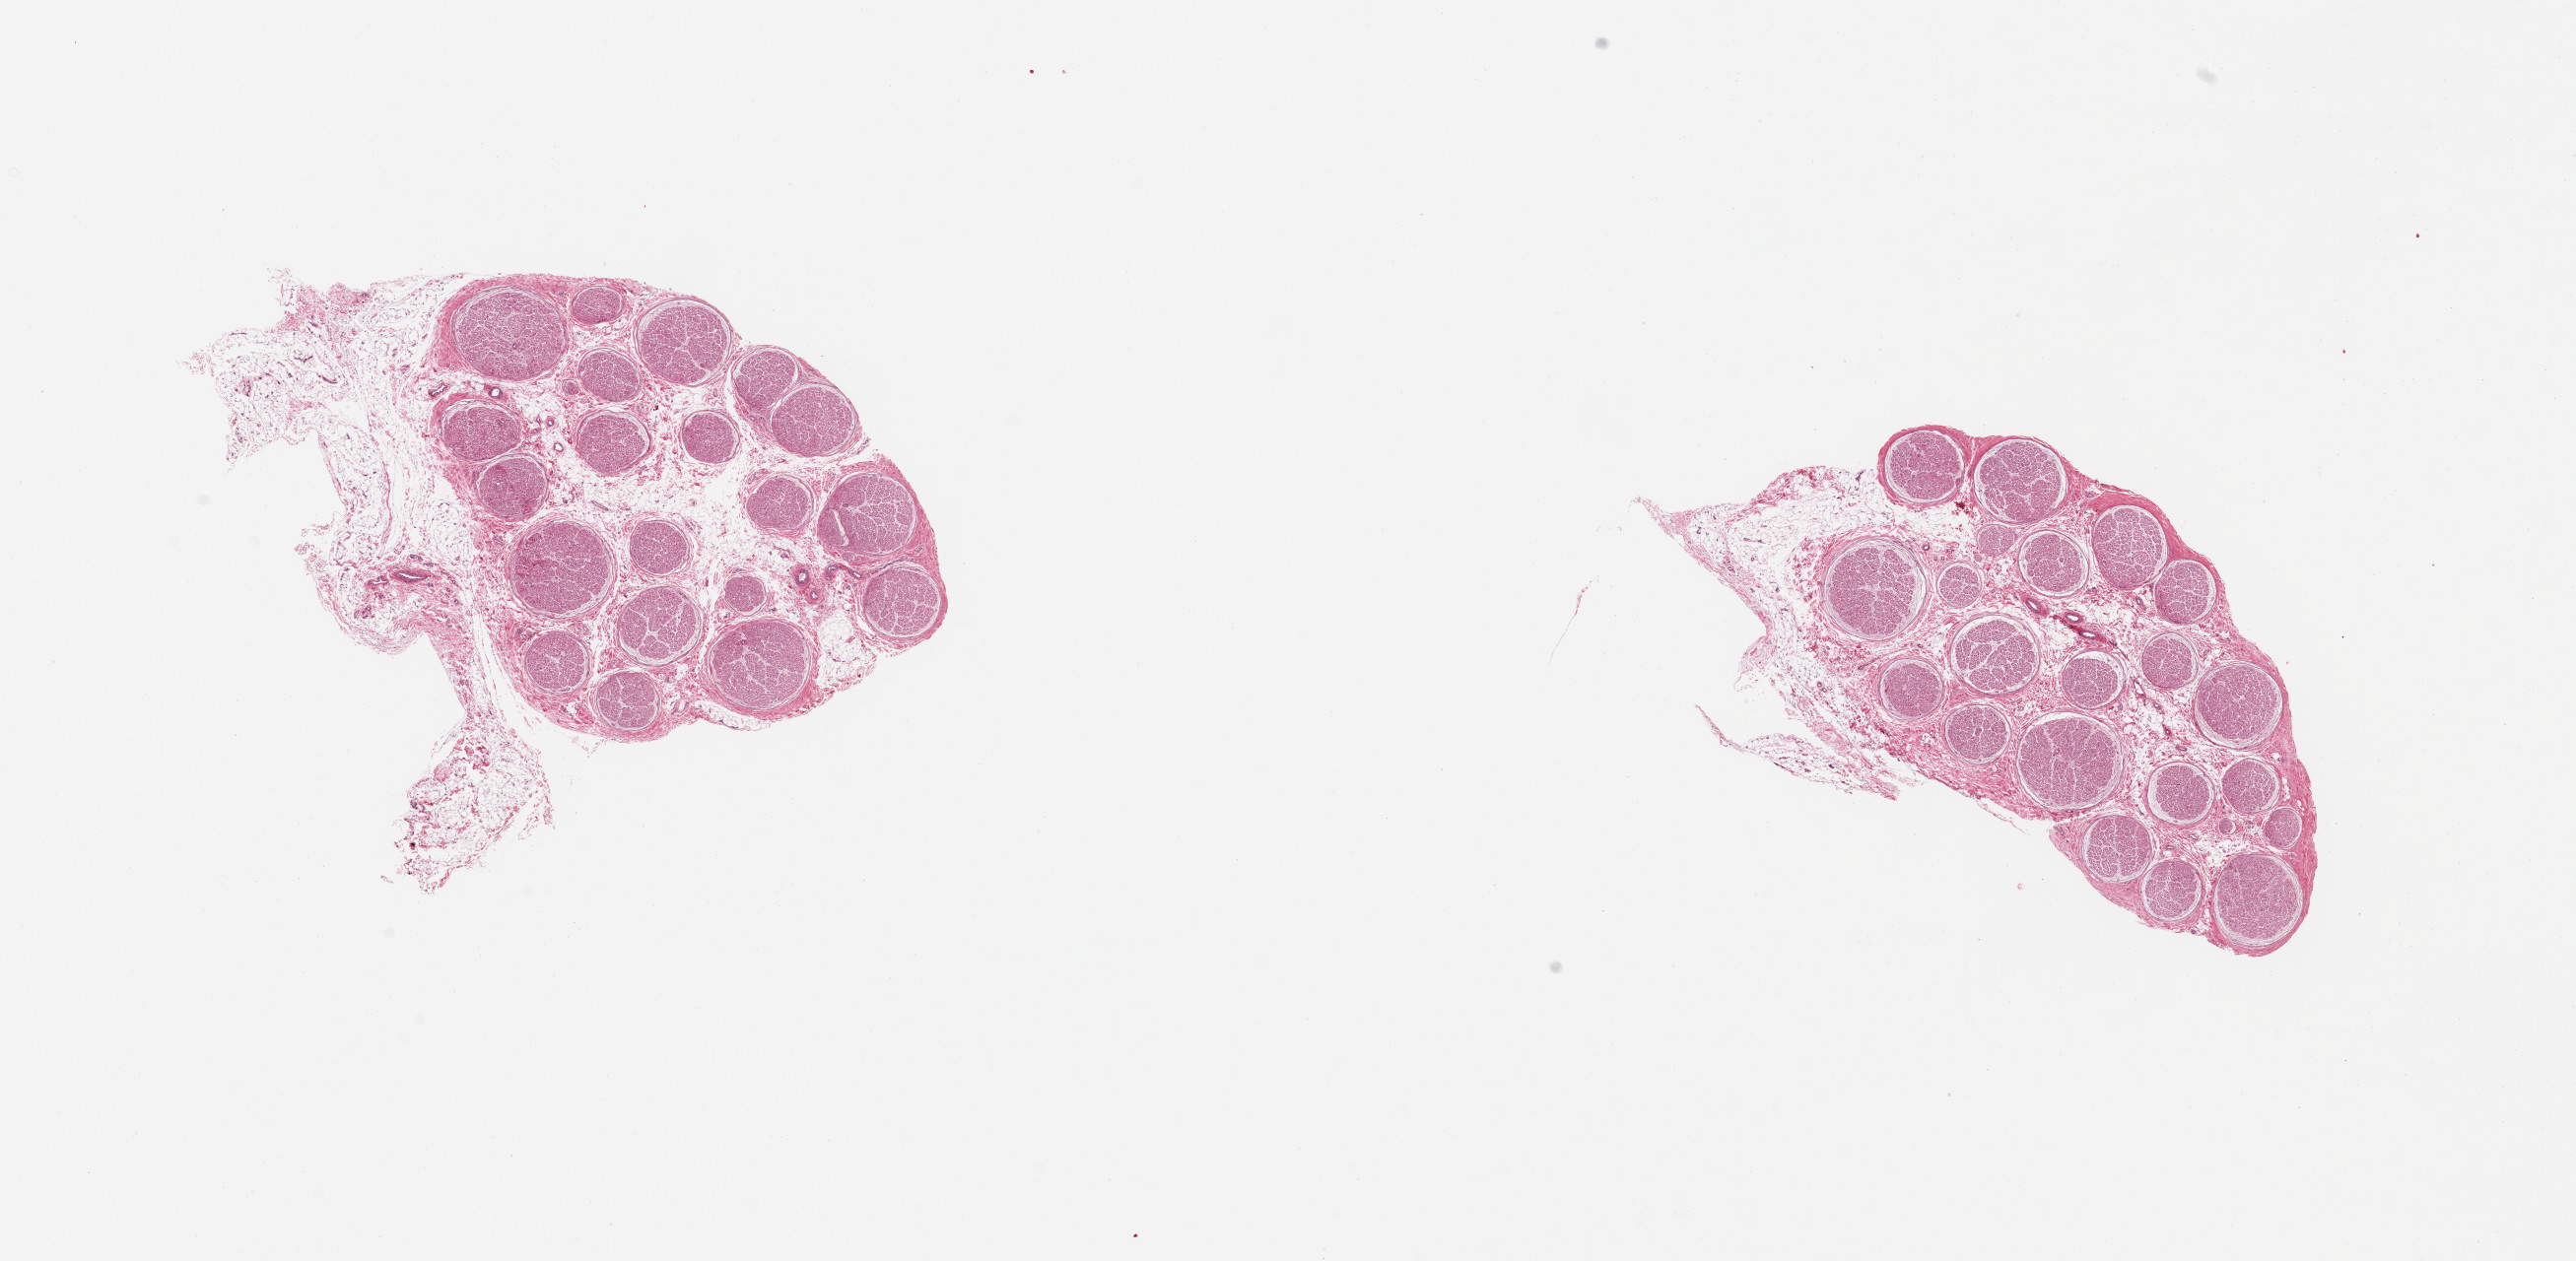
Hematoxylin and eosin (H&E) whole-slide image — whole scanned area (about 20.7 x 10.1 mm) shown as a low-resolution overview, PAXgene-fixed paraffin-embedded (PFPE) section, sampled site (target tissue): tibial nerve, donor tissue sample. Donor sex: female.
• pathologist's review note for this sample: 2 pieces; both include residual attached fat, up to 1.8 x 4.6 mm on one piece